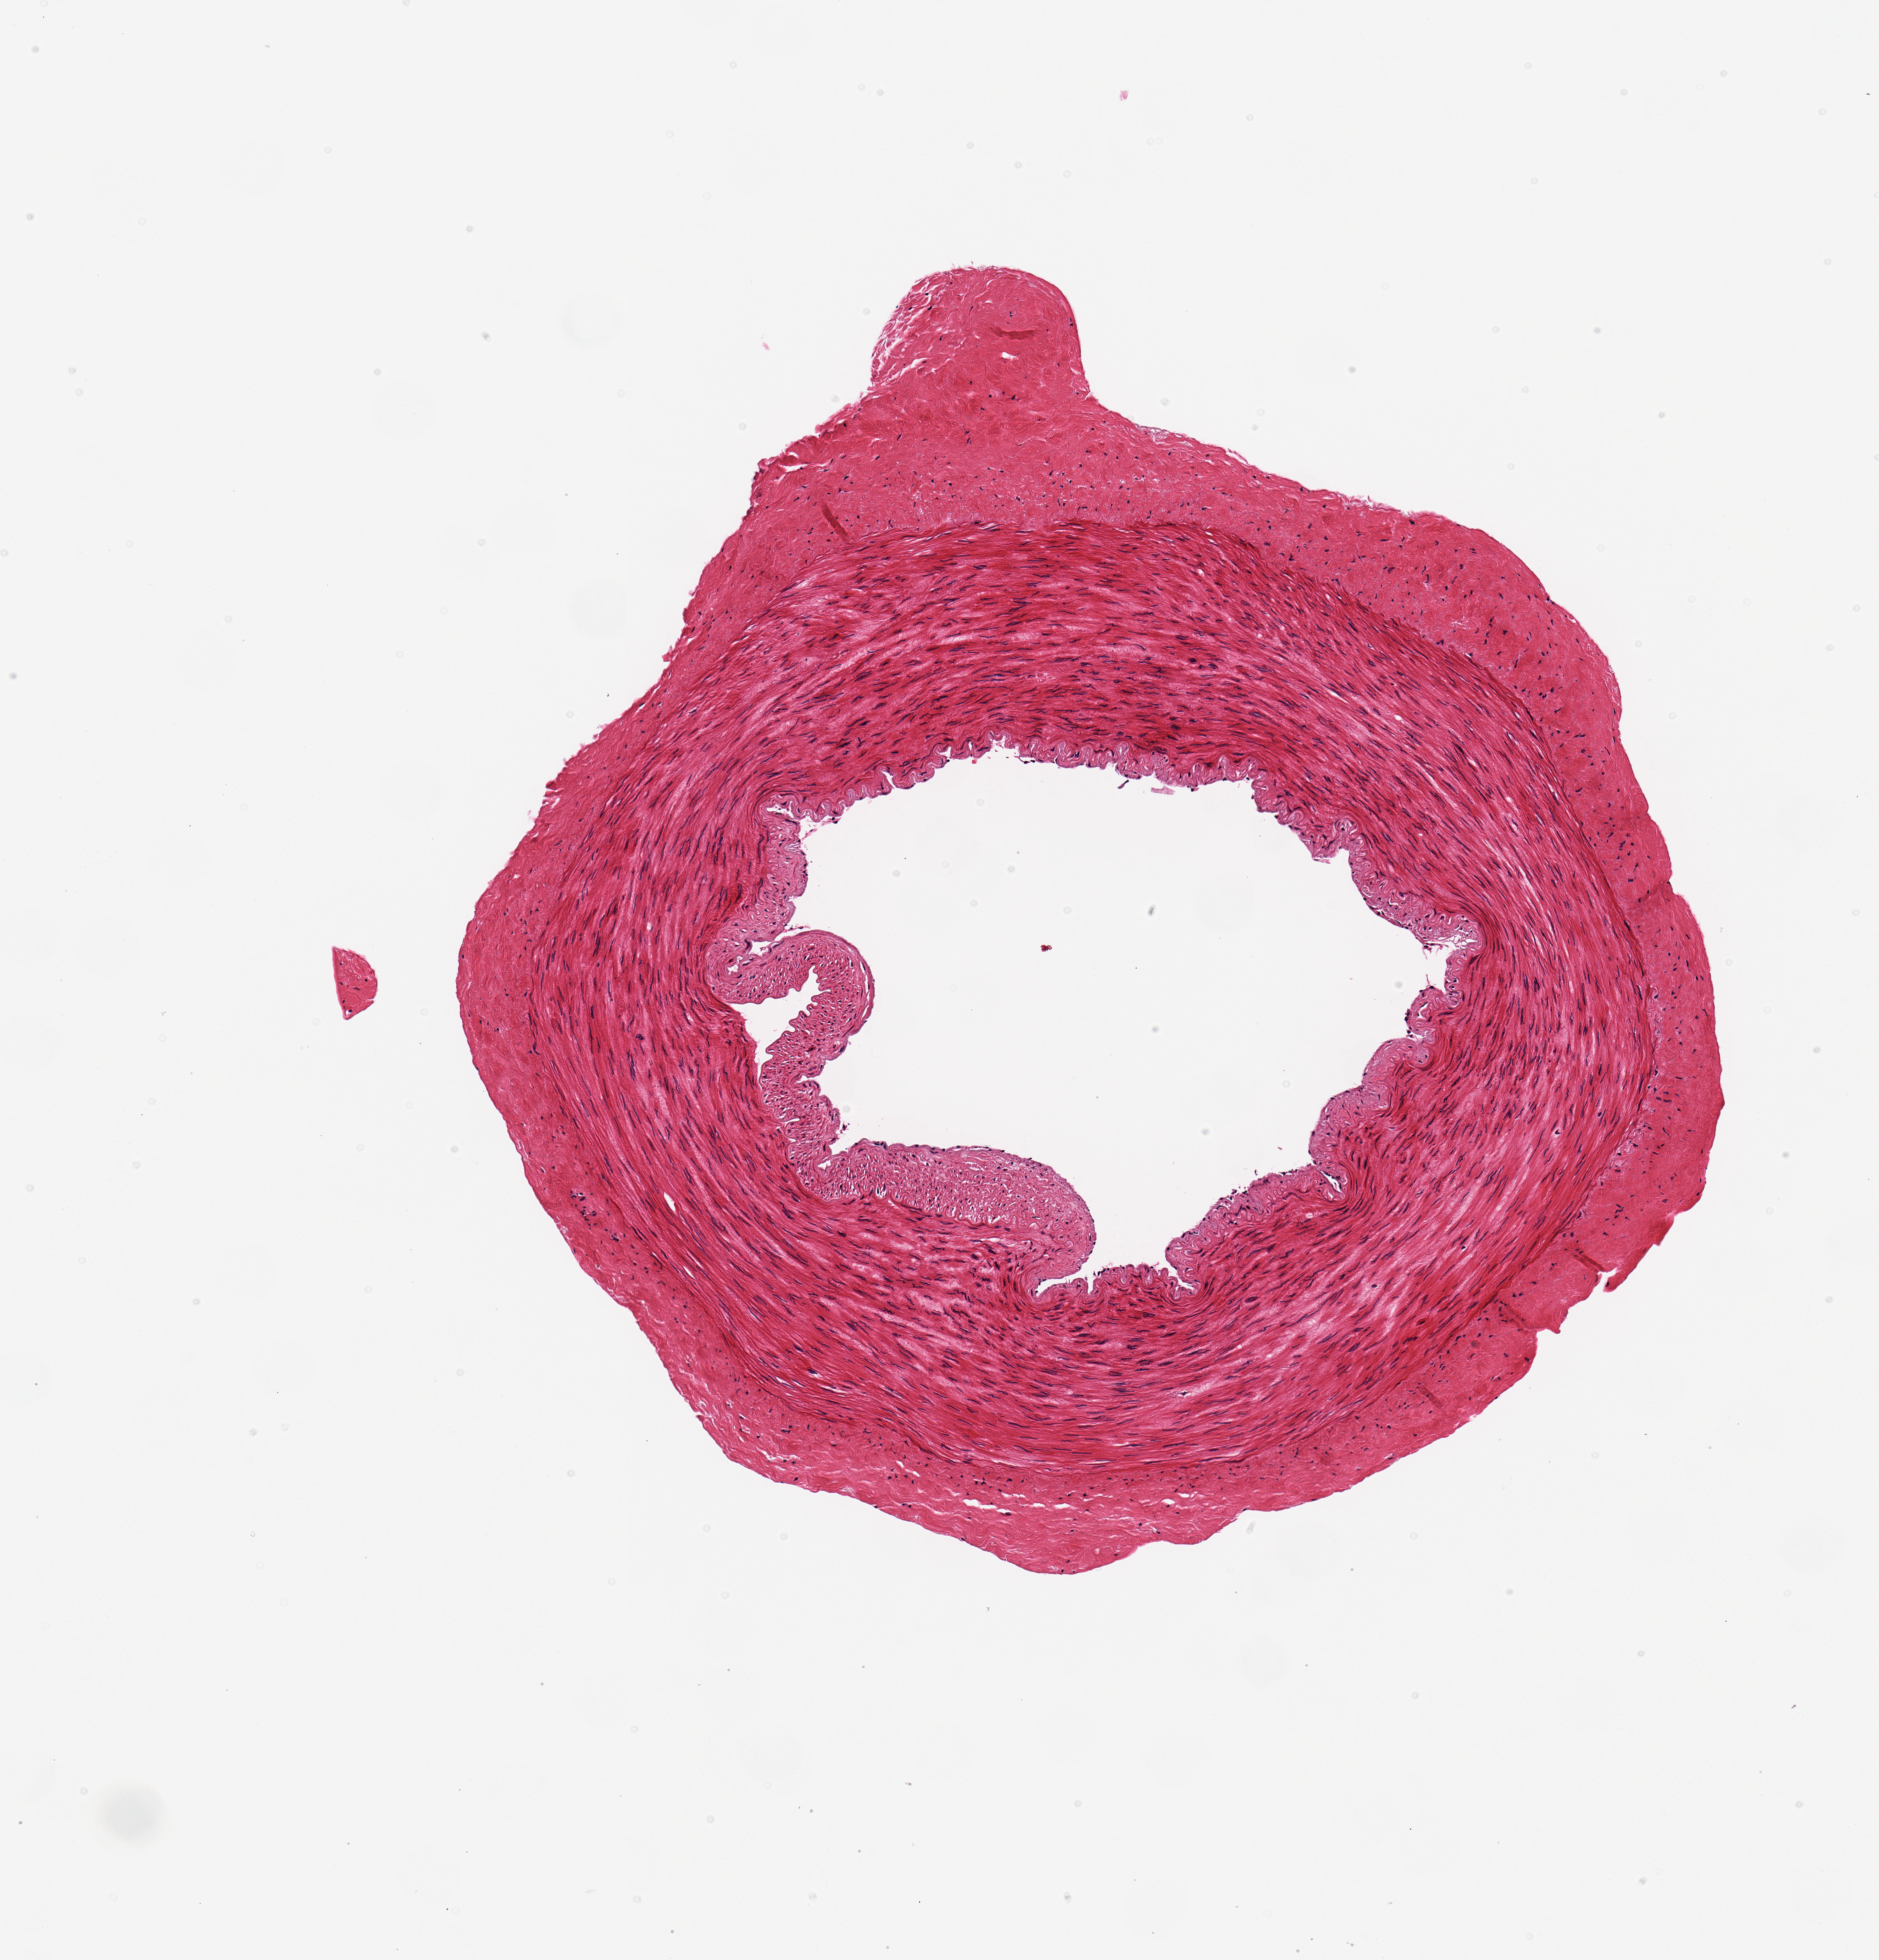
Haematoxylin and eosin whole-slide image — the whole scanned area (about 3.0 x 3.1 mm) at the scan's own resolution. PAXgene-fixed, paraffin-embedded tissue. Sampled site (target tissue): tibial artery. Tissue donor sample. Donor sex: male.
Pathologist's review note for this sample: 1.8x1.8mm. Good clean specimen.